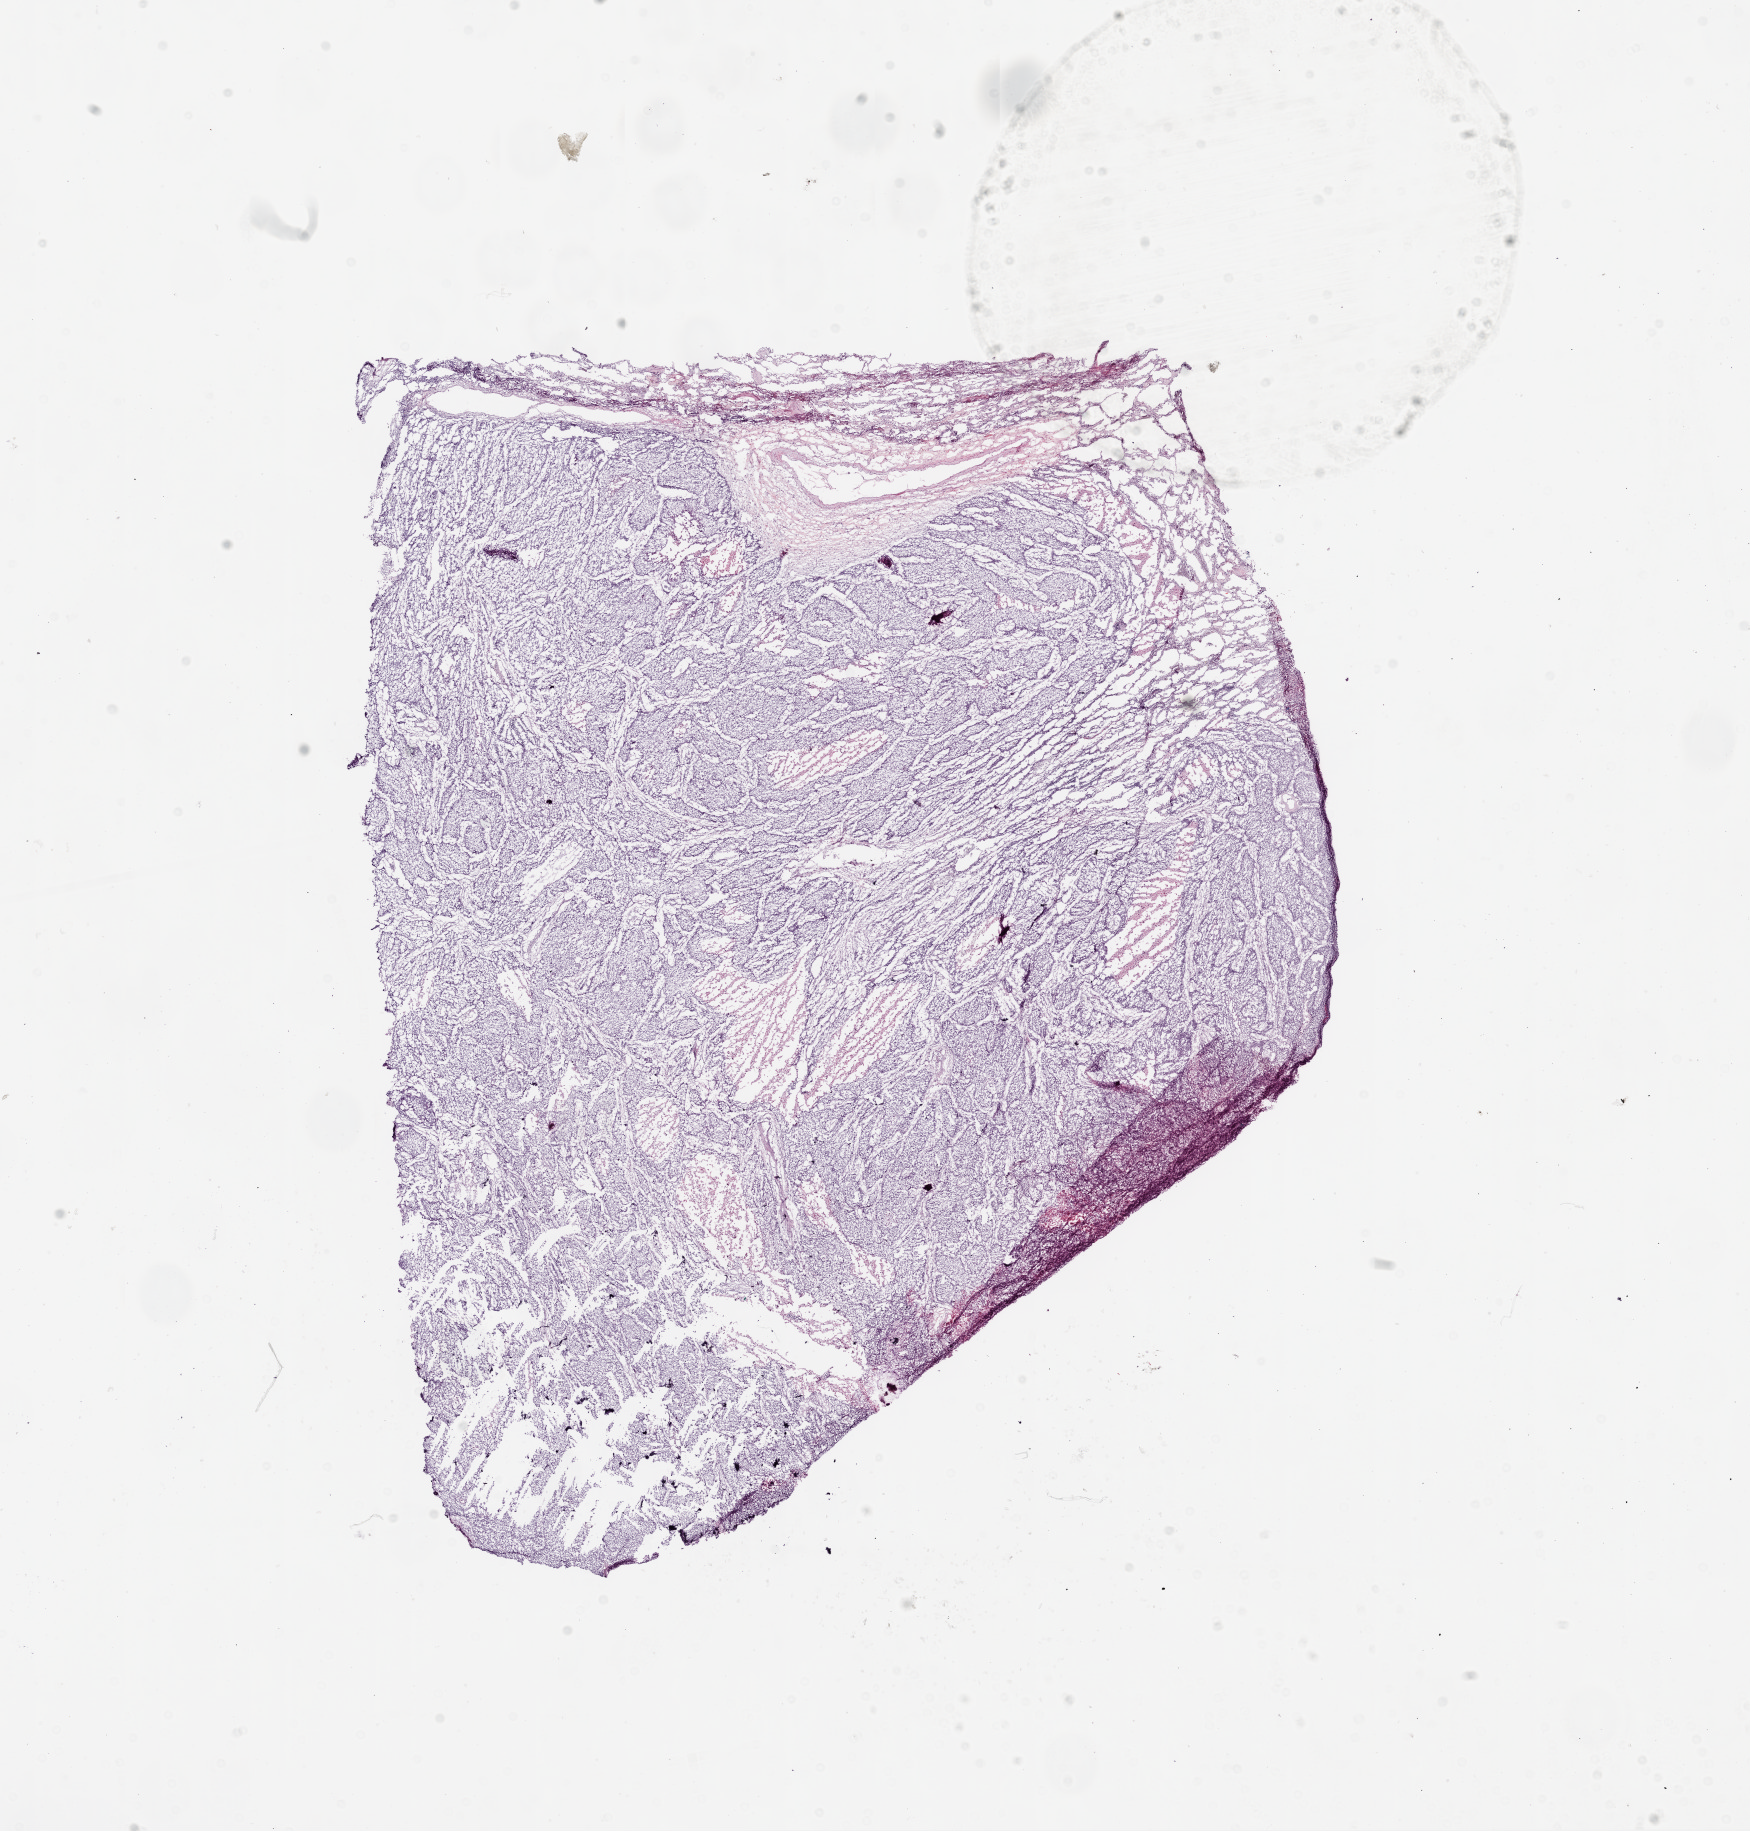
Whole-slide histology image, H&E, a low-resolution overview of the entire scanned area, about 14.0 x 14.7 mm. Frozen section from the top of the tissue portion. Sample: primary tumour, lung. Patient: female, age at initial diagnosis 64 years. Slide review estimates, as recorded: tumour cells 80%, tumour nuclei 85%, normal cells 5%, stromal cells 10%, necrosis 5%.
* AJCC pathologic stage: IB
* pathologic diagnosis: Squamous cell carcinoma, NOS